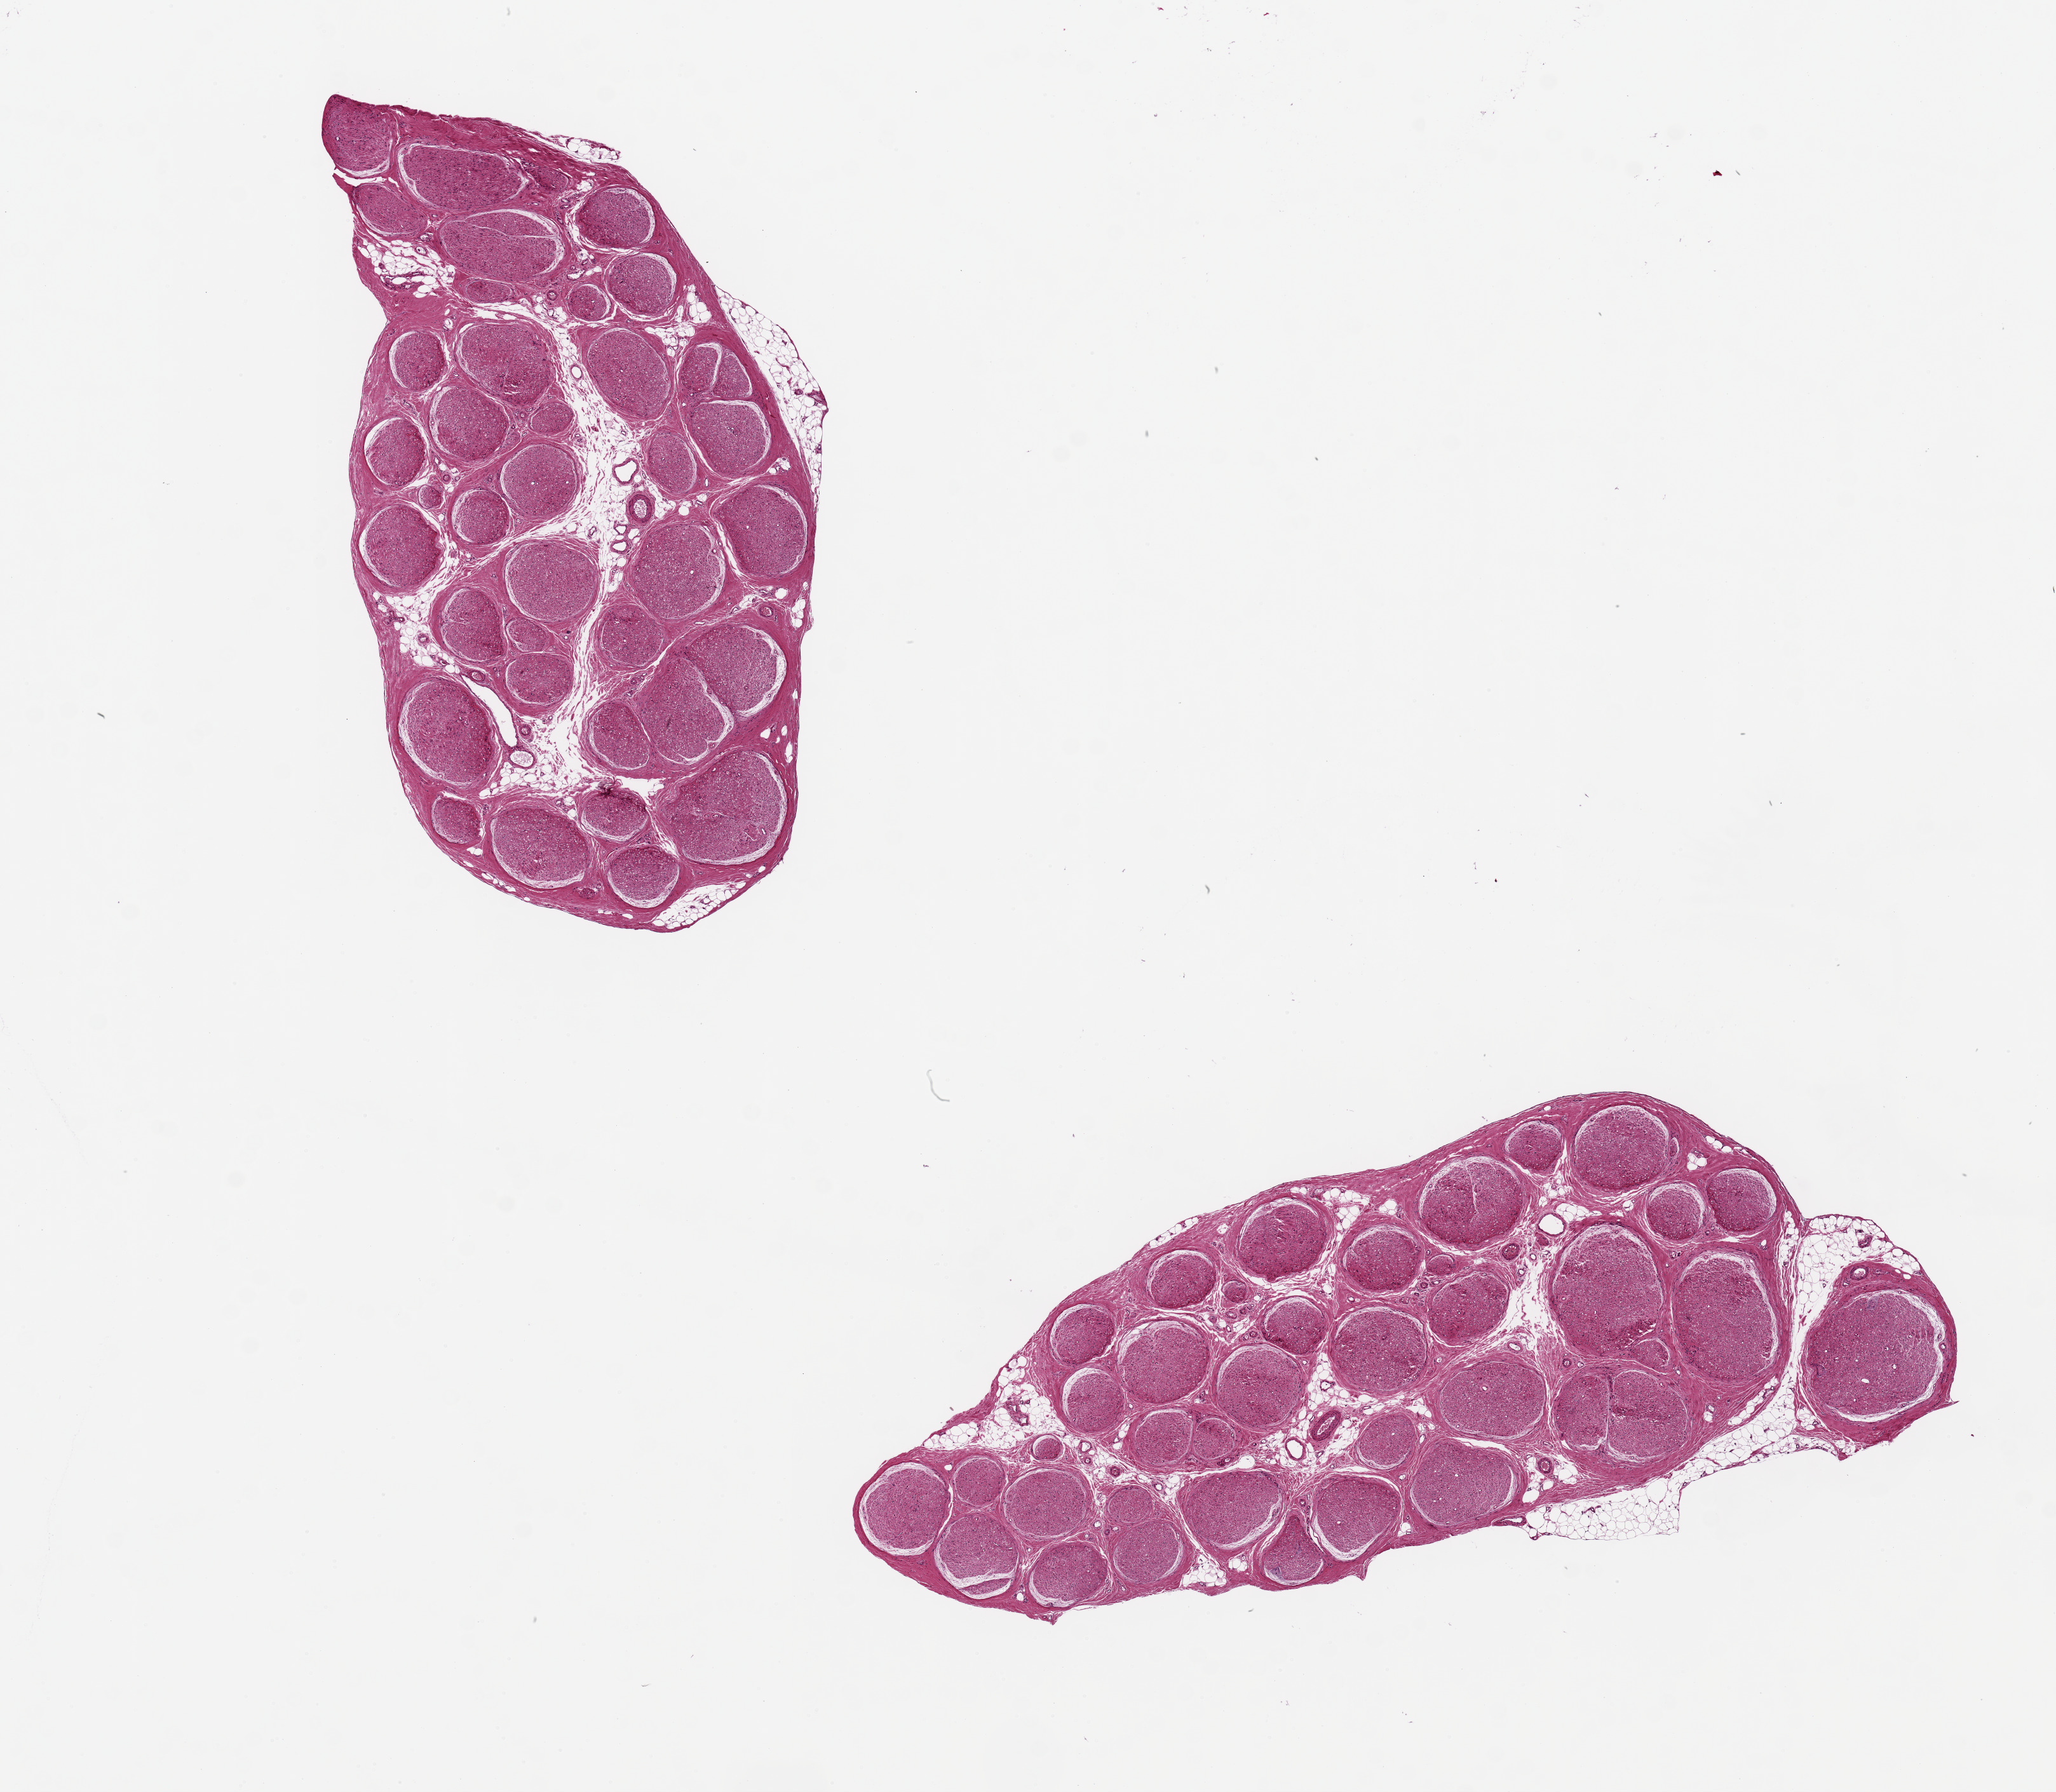
Digitized hematoxylin and eosin (H&E)-stained section — whole scanned area (about 12.8 x 11.2 mm) shown as a low-resolution overview, PAXgene-fixed, paraffin-embedded tissue, sampled site (target tissue): tibial nerve, donor tissue sample. Donor: female.
Review note (as recorded): 2 pieces ~4mm d. Good clean specimens.